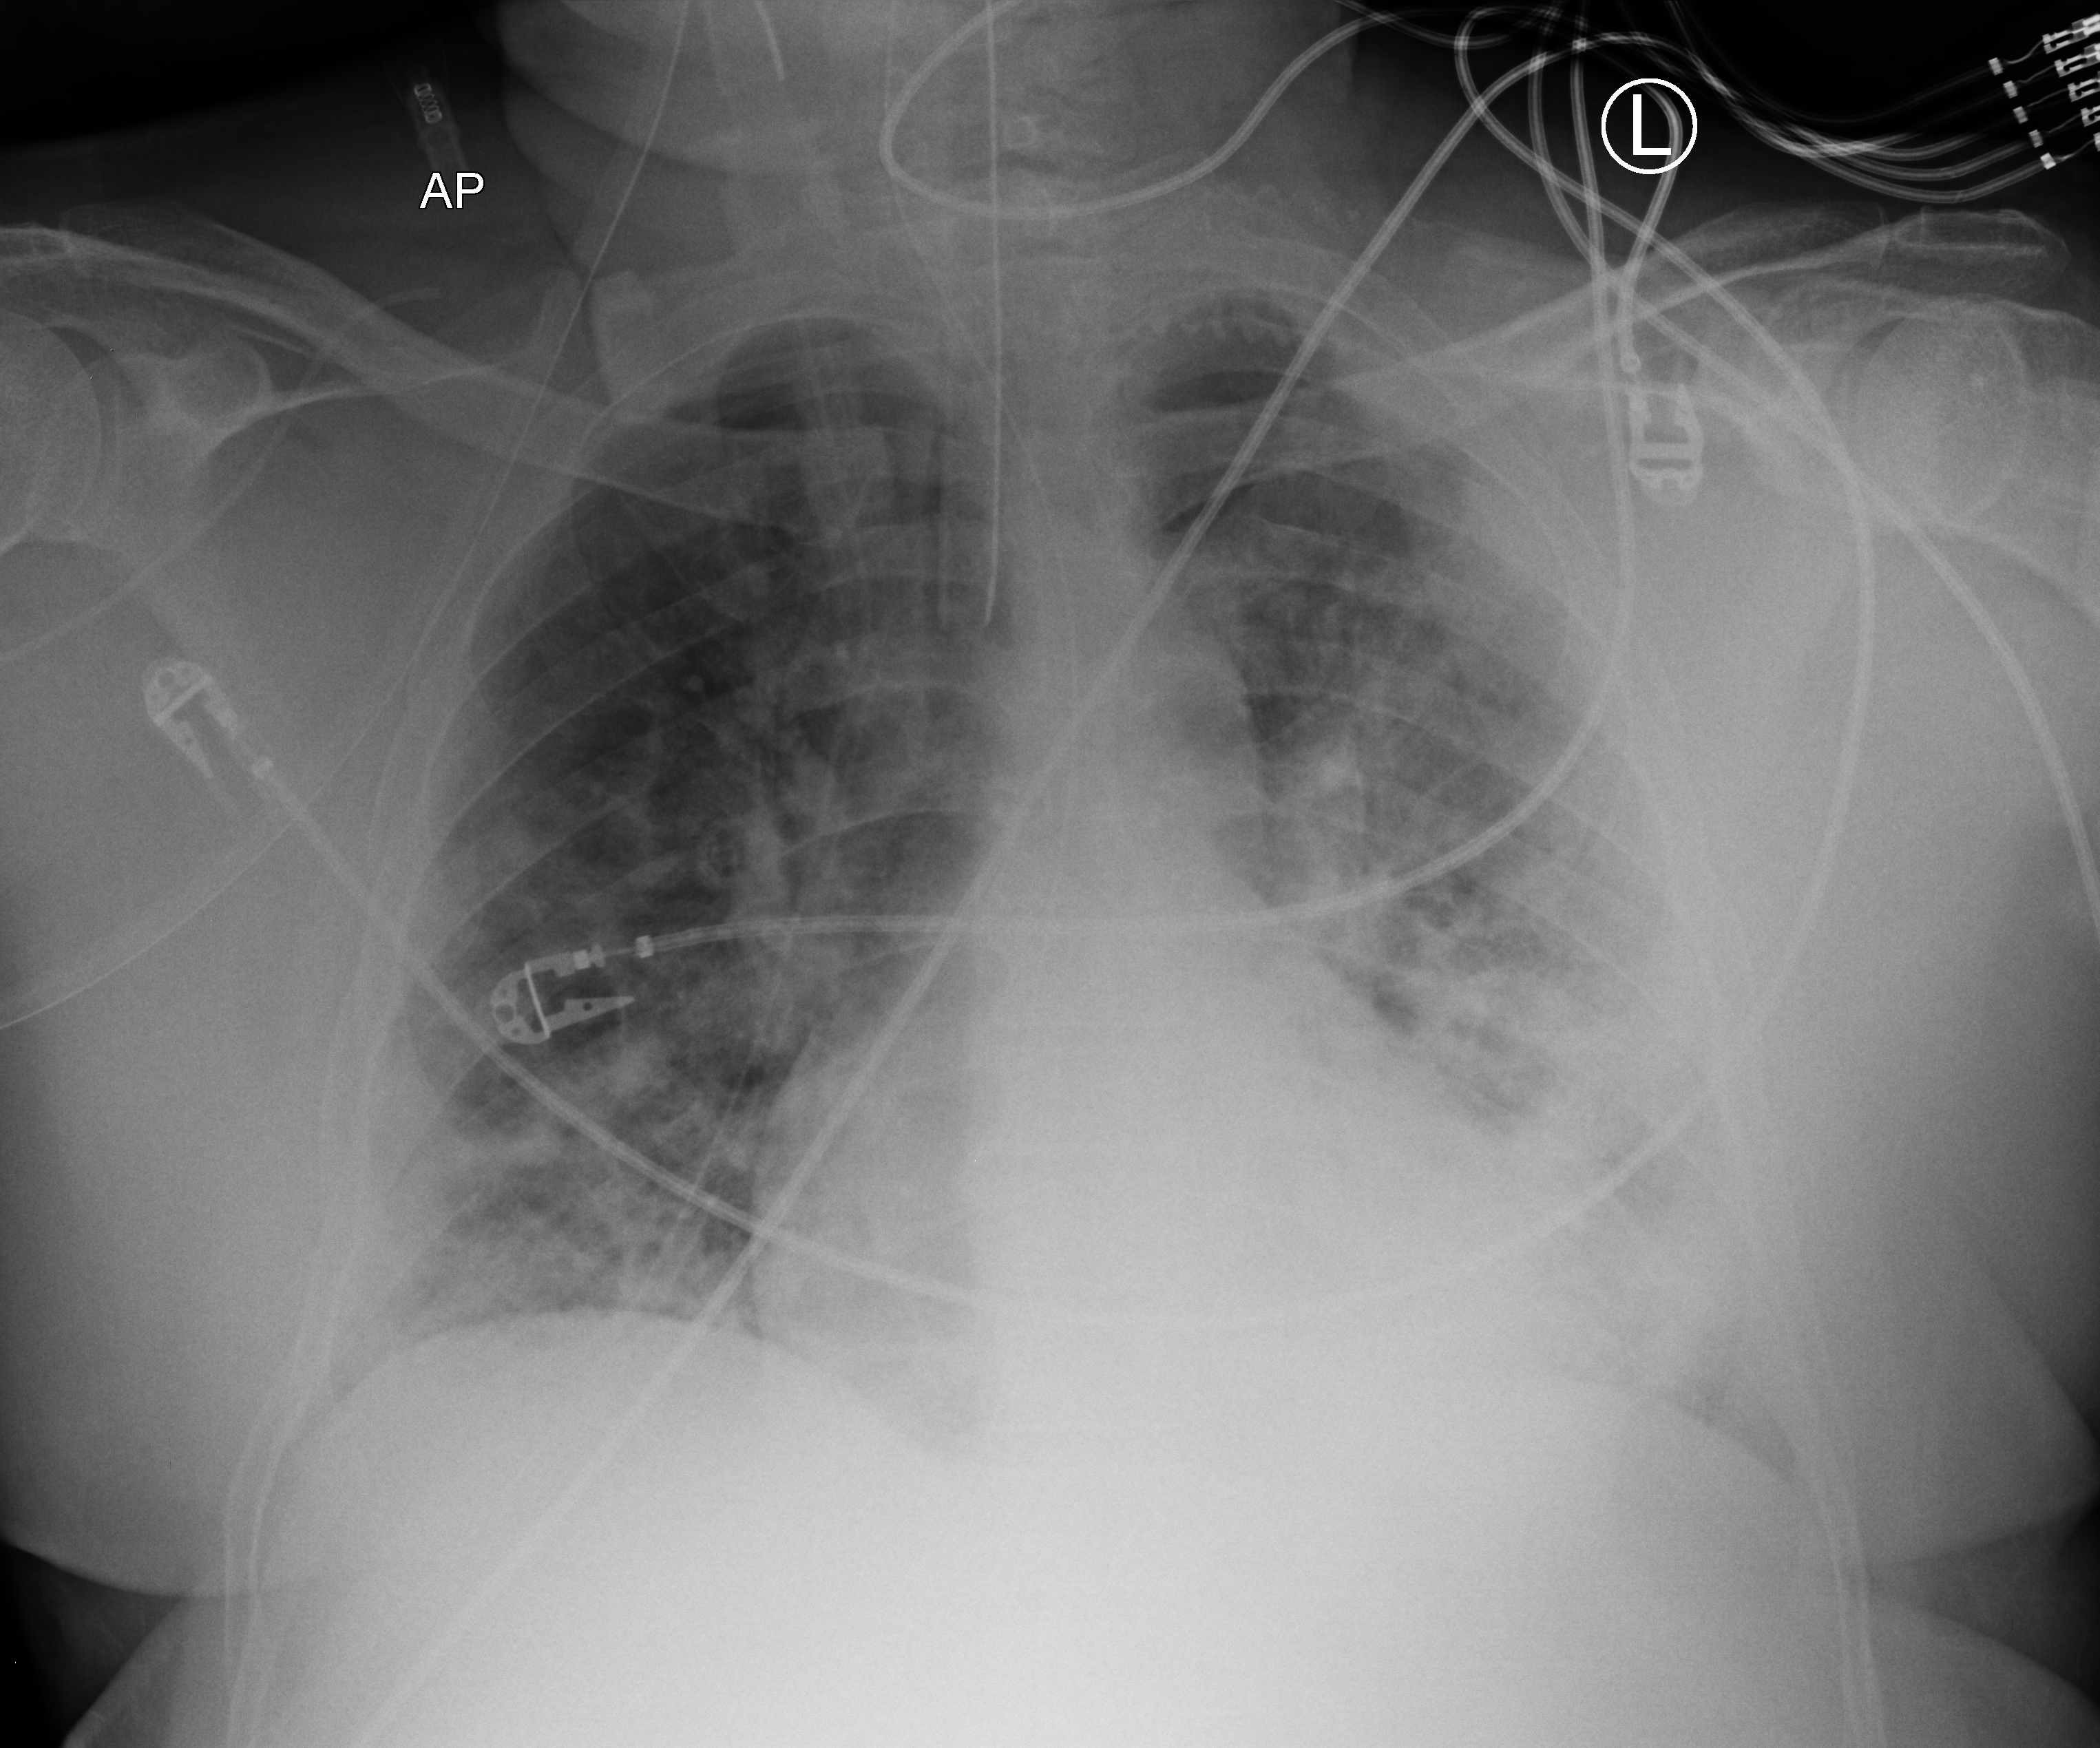
Bedside chest radiograph (computed radiography), anteroposterior (AP) projection. Male patient hospitalised with COVID-19, age 18–59 years.
Hospital-stay facts (about this admission, not read from this image; timing relative to this image not recorded): chronic kidney disease (admission record): no; admitted to intensive care during this hospital stay: yes; hypertension (admission record): no.